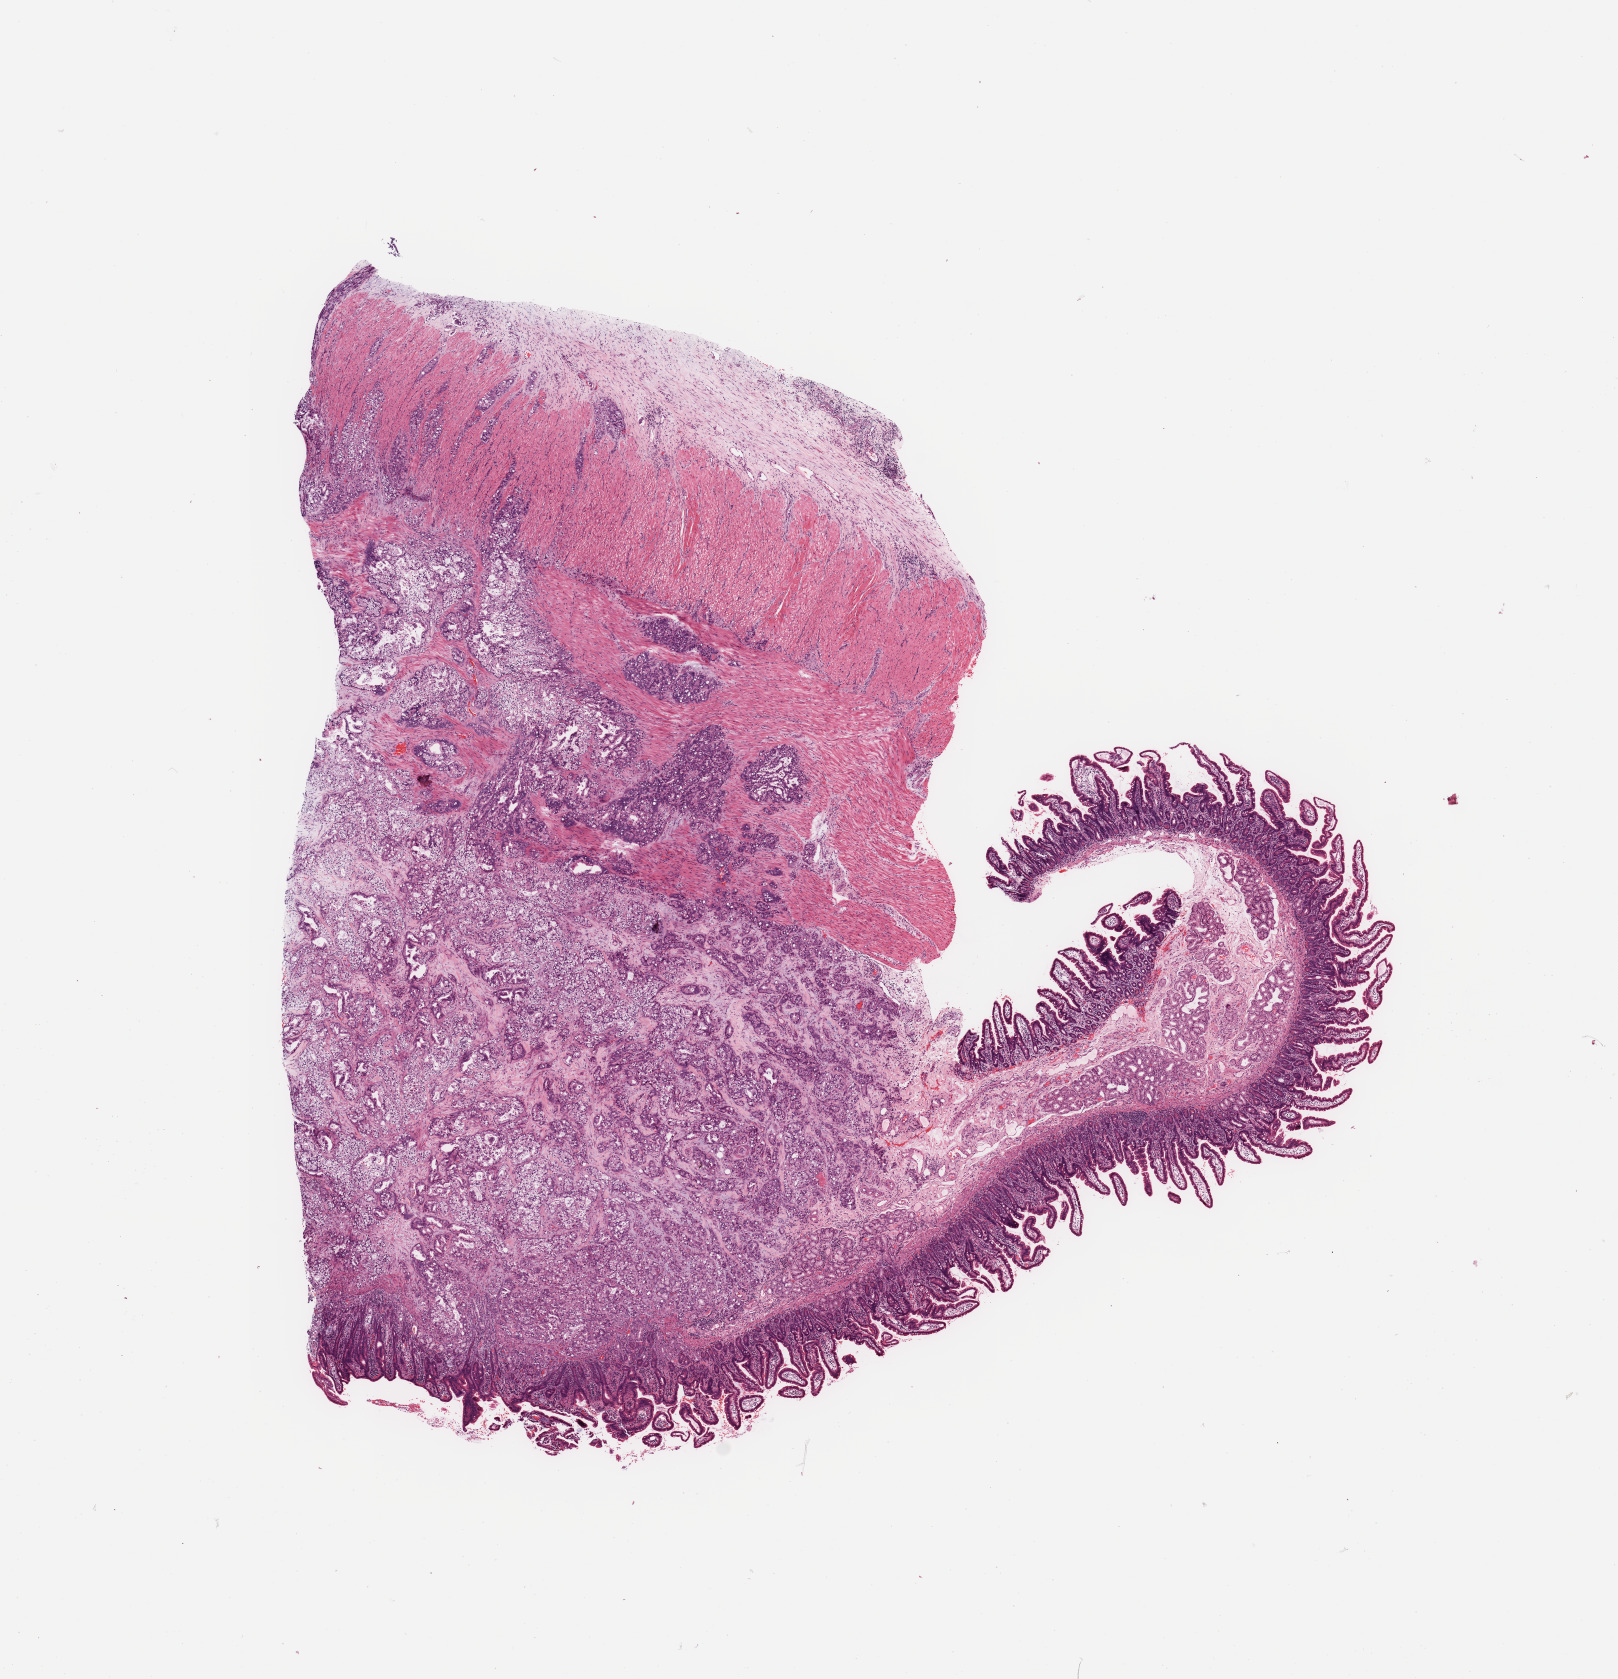
Digitized H&E-stained tissue section (whole slide) — whole scanned area (about 12.8 x 13.3 mm, slide scanned at 20x) shown as a low-resolution overview, tumour tissue sample, sampled site: pancreas. Female, 60 y/o. Composition of this section per pathologist review: tumour nuclei 70%, necrosis 0%.
Diagnosis: Infiltrating duct carcinoma, NOS.